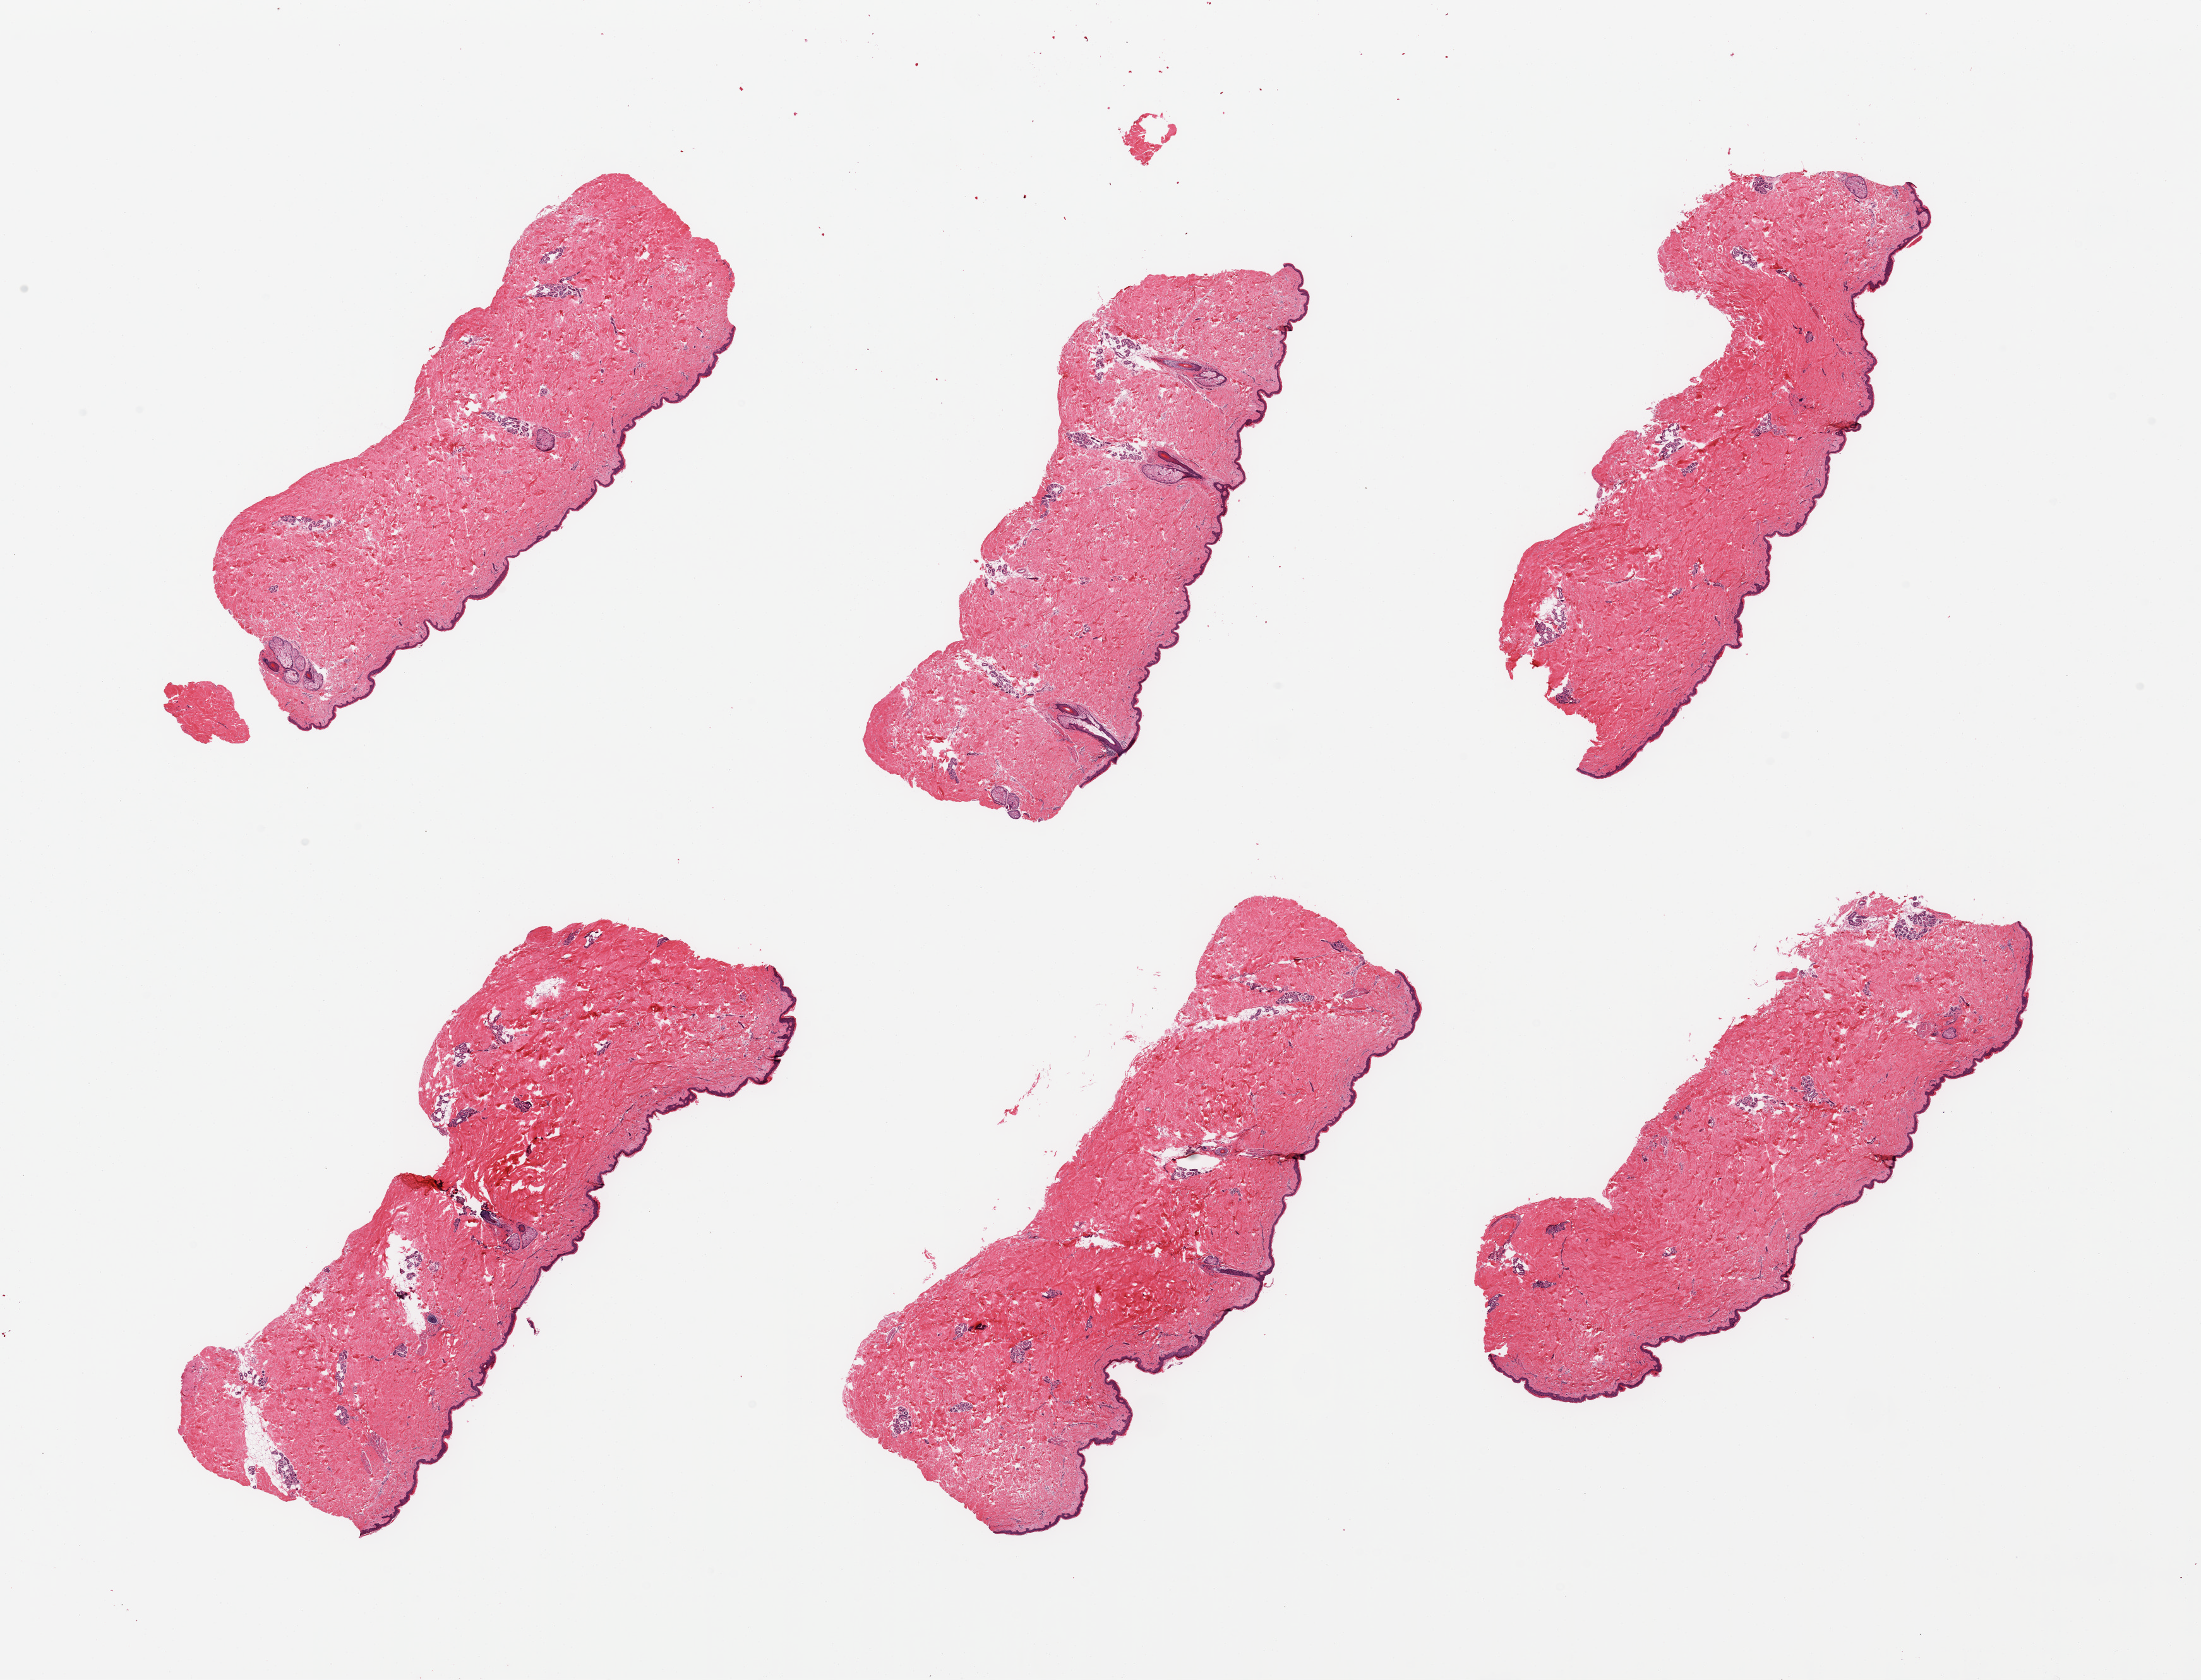
Digitized haematoxylin and eosin-stained section, brightfield, shown as a low-resolution overview of the whole scanned area (about 27.6 x 21.0 mm), PAXgene-fixed paraffin-embedded (PFPE) section, sampled site (target tissue): skin of suprapubic region, tissue donor sample. Female donor.
Pathologist's review note for this sample: 6 pieces, no dermal fat; squamous epithelium is ~35 microns.